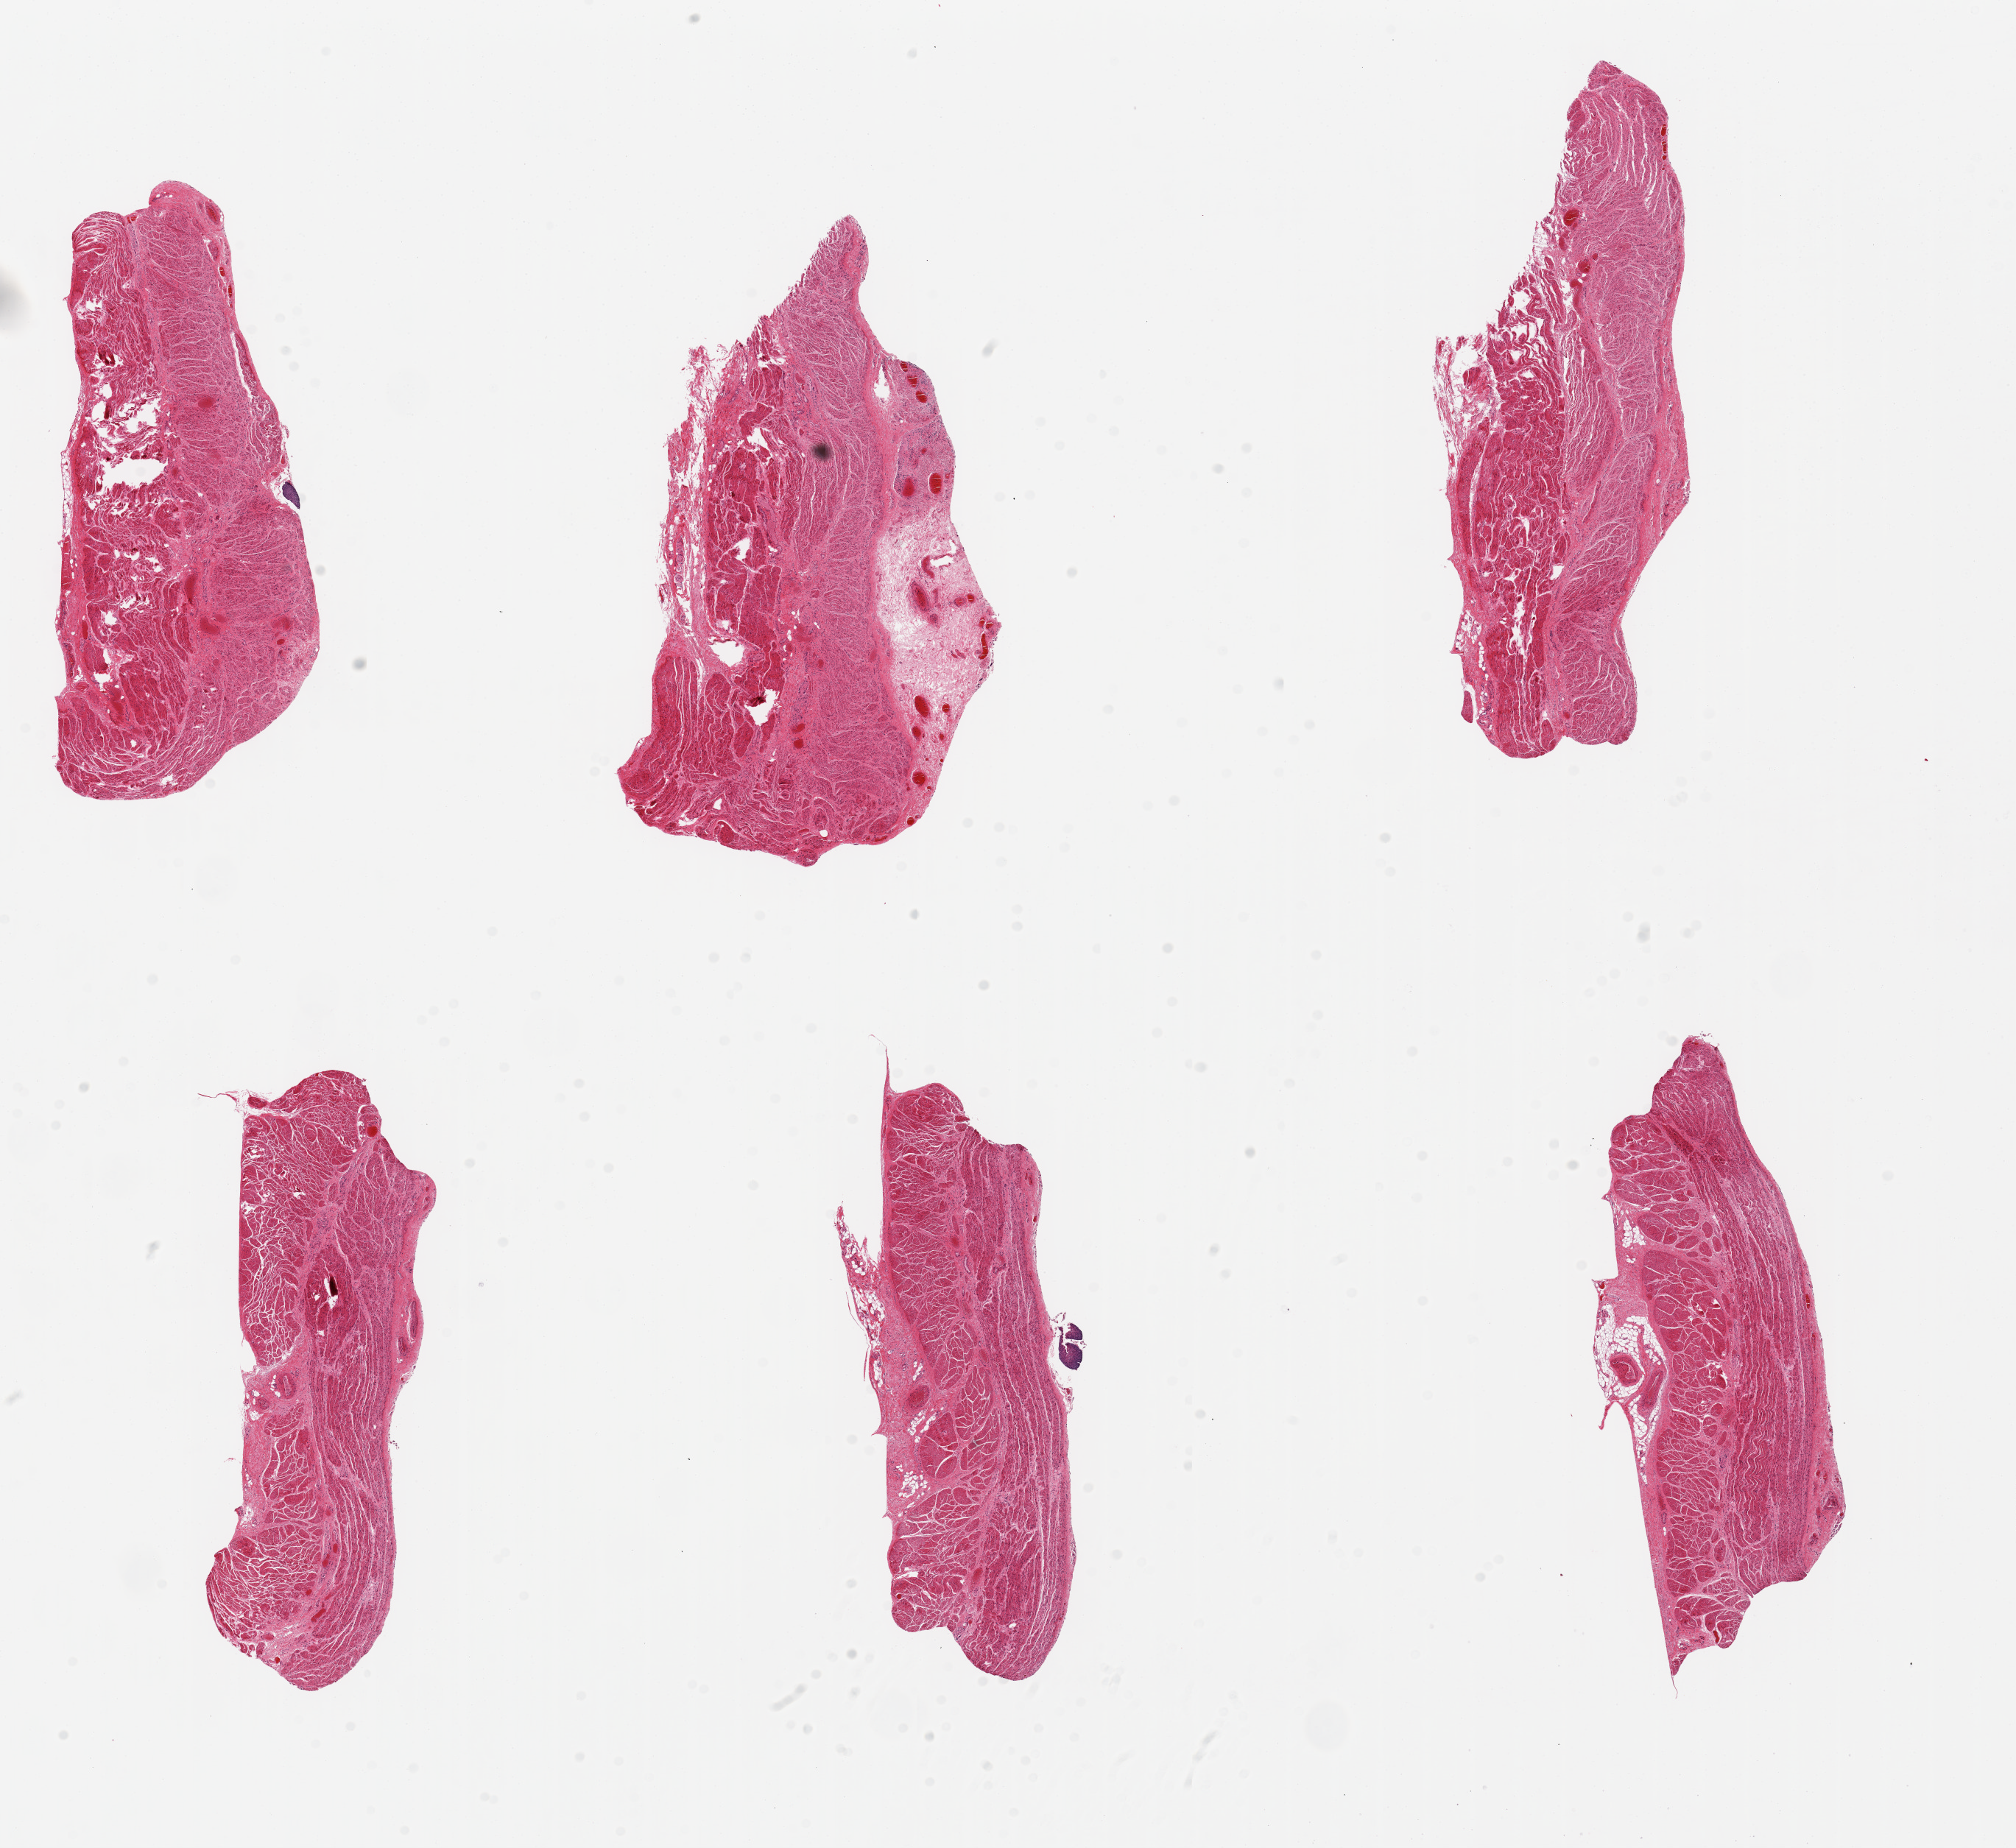
Digitized haematoxylin and eosin-stained section, brightfield — whole scanned area (about 21.7 x 19.9 mm) shown as a low-resolution overview, PAXgene-fixed paraffin-embedded (PFPE) section, section of gastroesophageal junction (target tissue), donor tissue sample. Donor: male.
• pathologist's review note for this sample: 6 pieces, up to 7.5x3mm; all muscularis, good specimens